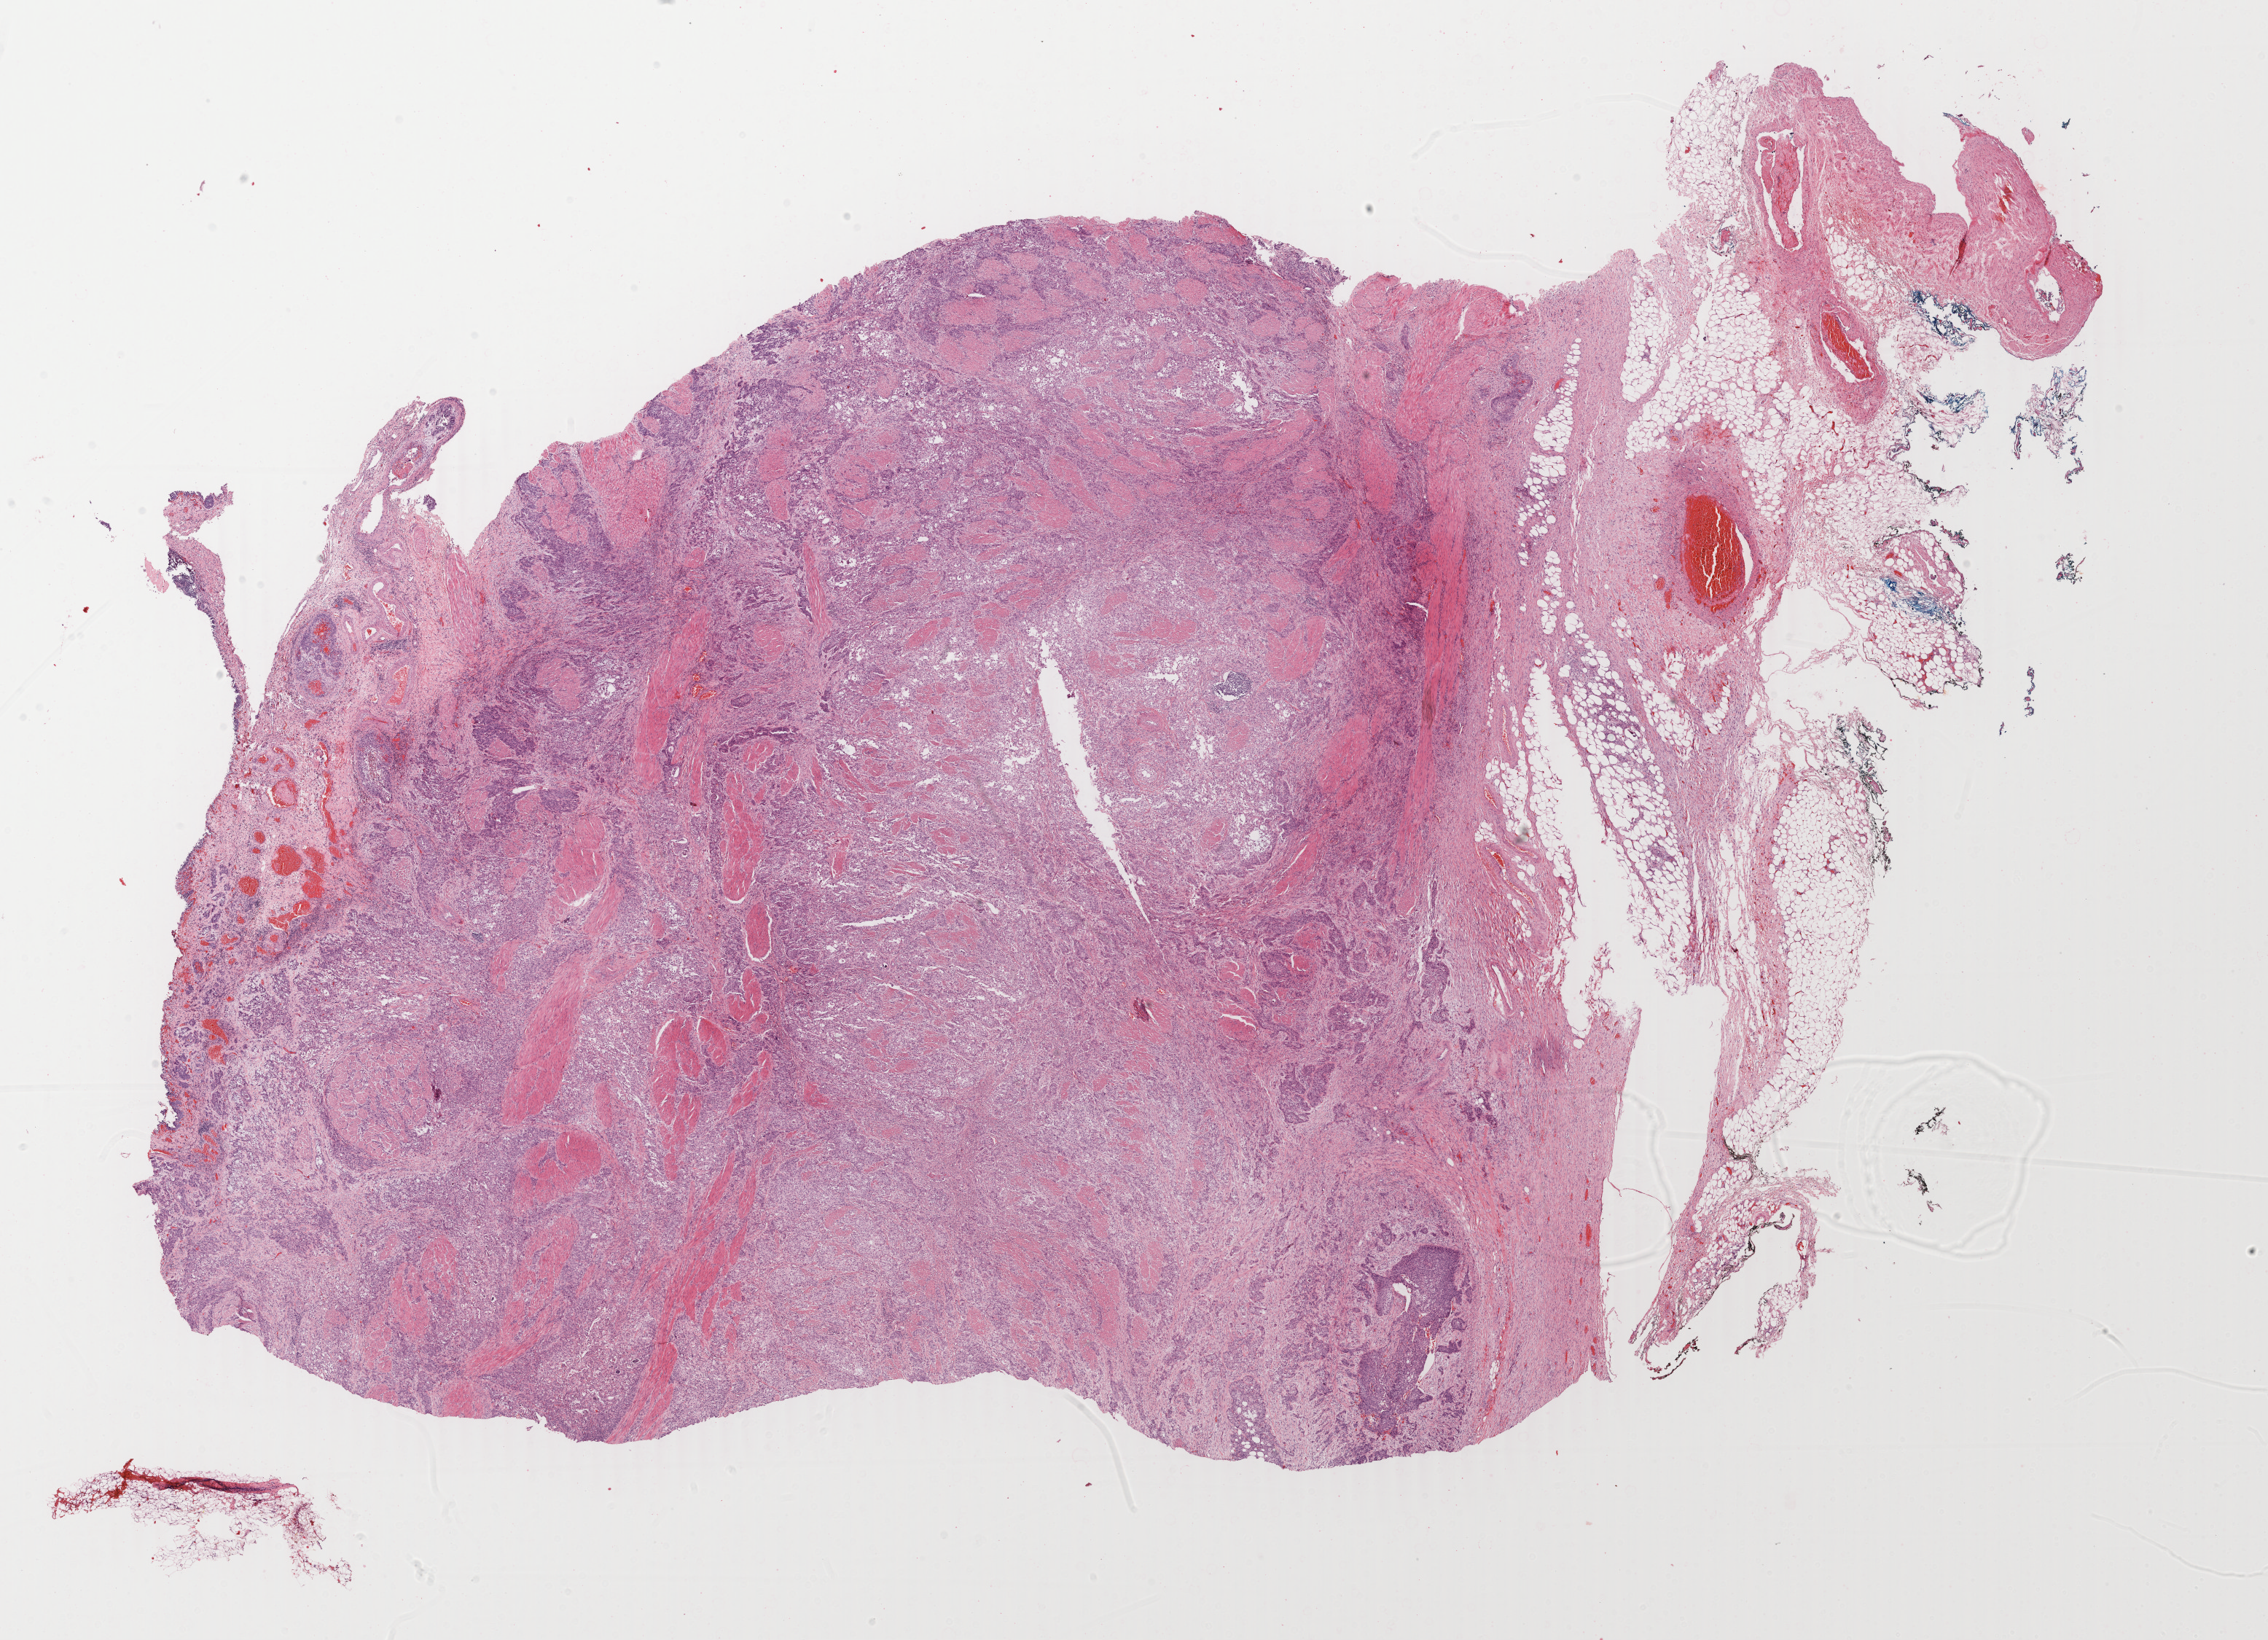
Whole-slide histology image, Hematoxylin and eosin (H&E) stained — low-resolution overview of the scanned area, about 24.7 x 17.9 mm (slide scanned at 40x), formalin-fixed paraffin-embedded (FFPE) diagnostic section, sample: primary tumour, bladder. Male, age 76 years at initial diagnosis. Histologic grade: high grade.
Histologic diagnosis: Transitional cell carcinoma (posterior wall of bladder). Lymph nodes positive (case pathology): 0 of 2 examined. AJCC pathologic stage: III (7th edition).